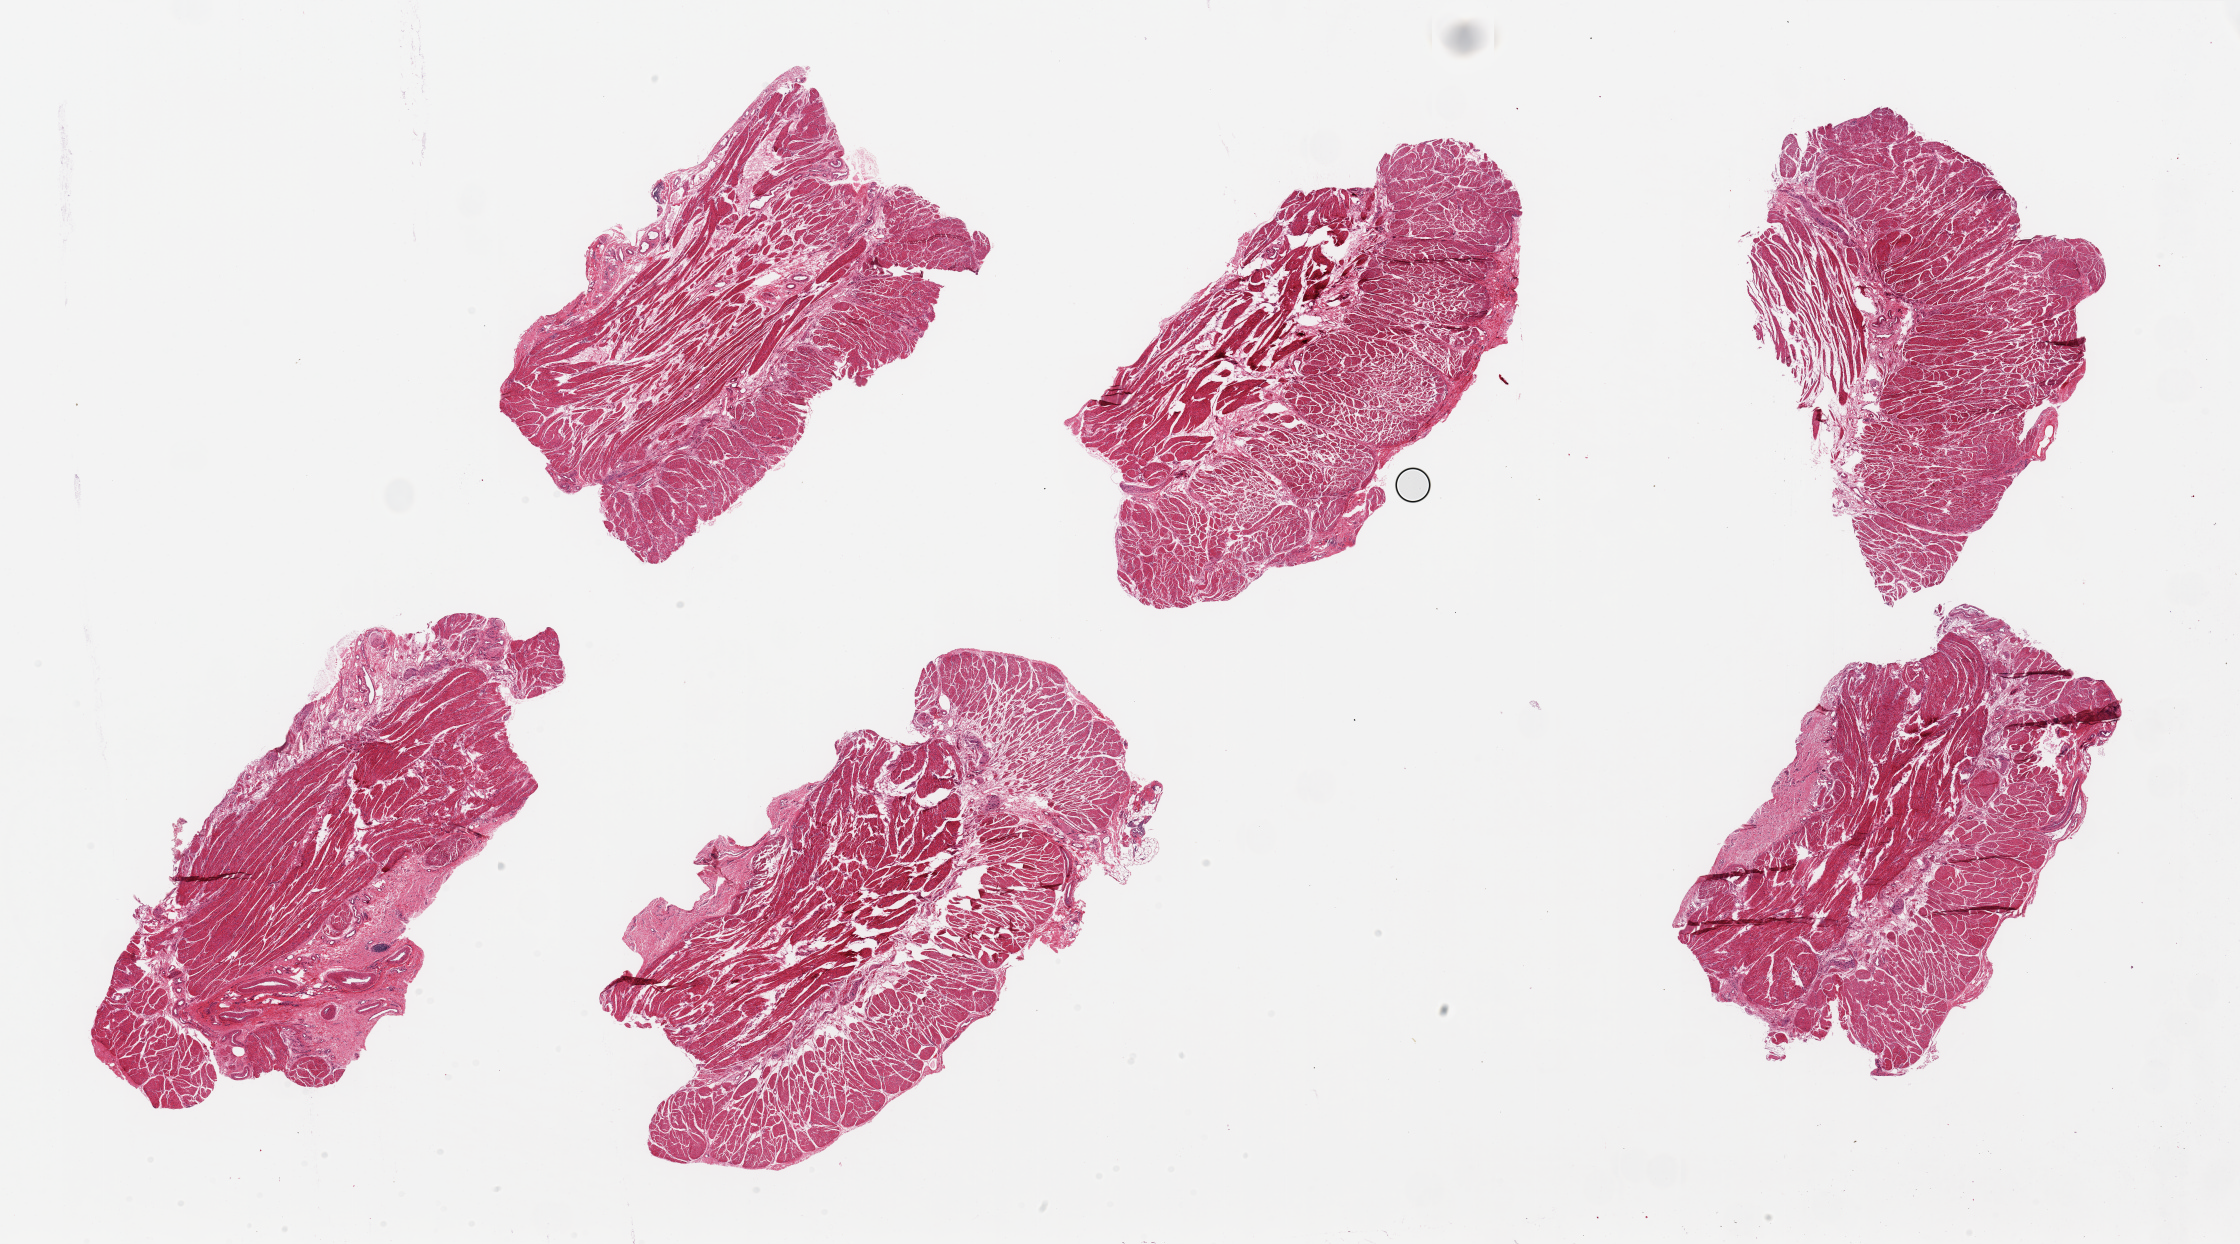
Digitized H&E-stained section, brightfield, a low-resolution overview of the entire scanned area, about 35.4 x 19.7 mm, PAXgene-fixed, paraffin-embedded tissue, target tissue: gastroesophageal junction, tissue donor sample. Male donor.
Reviewer comment on this tissue sample: 6 pieces, up to 10x5mm; essentially all muscularis, good specimens.